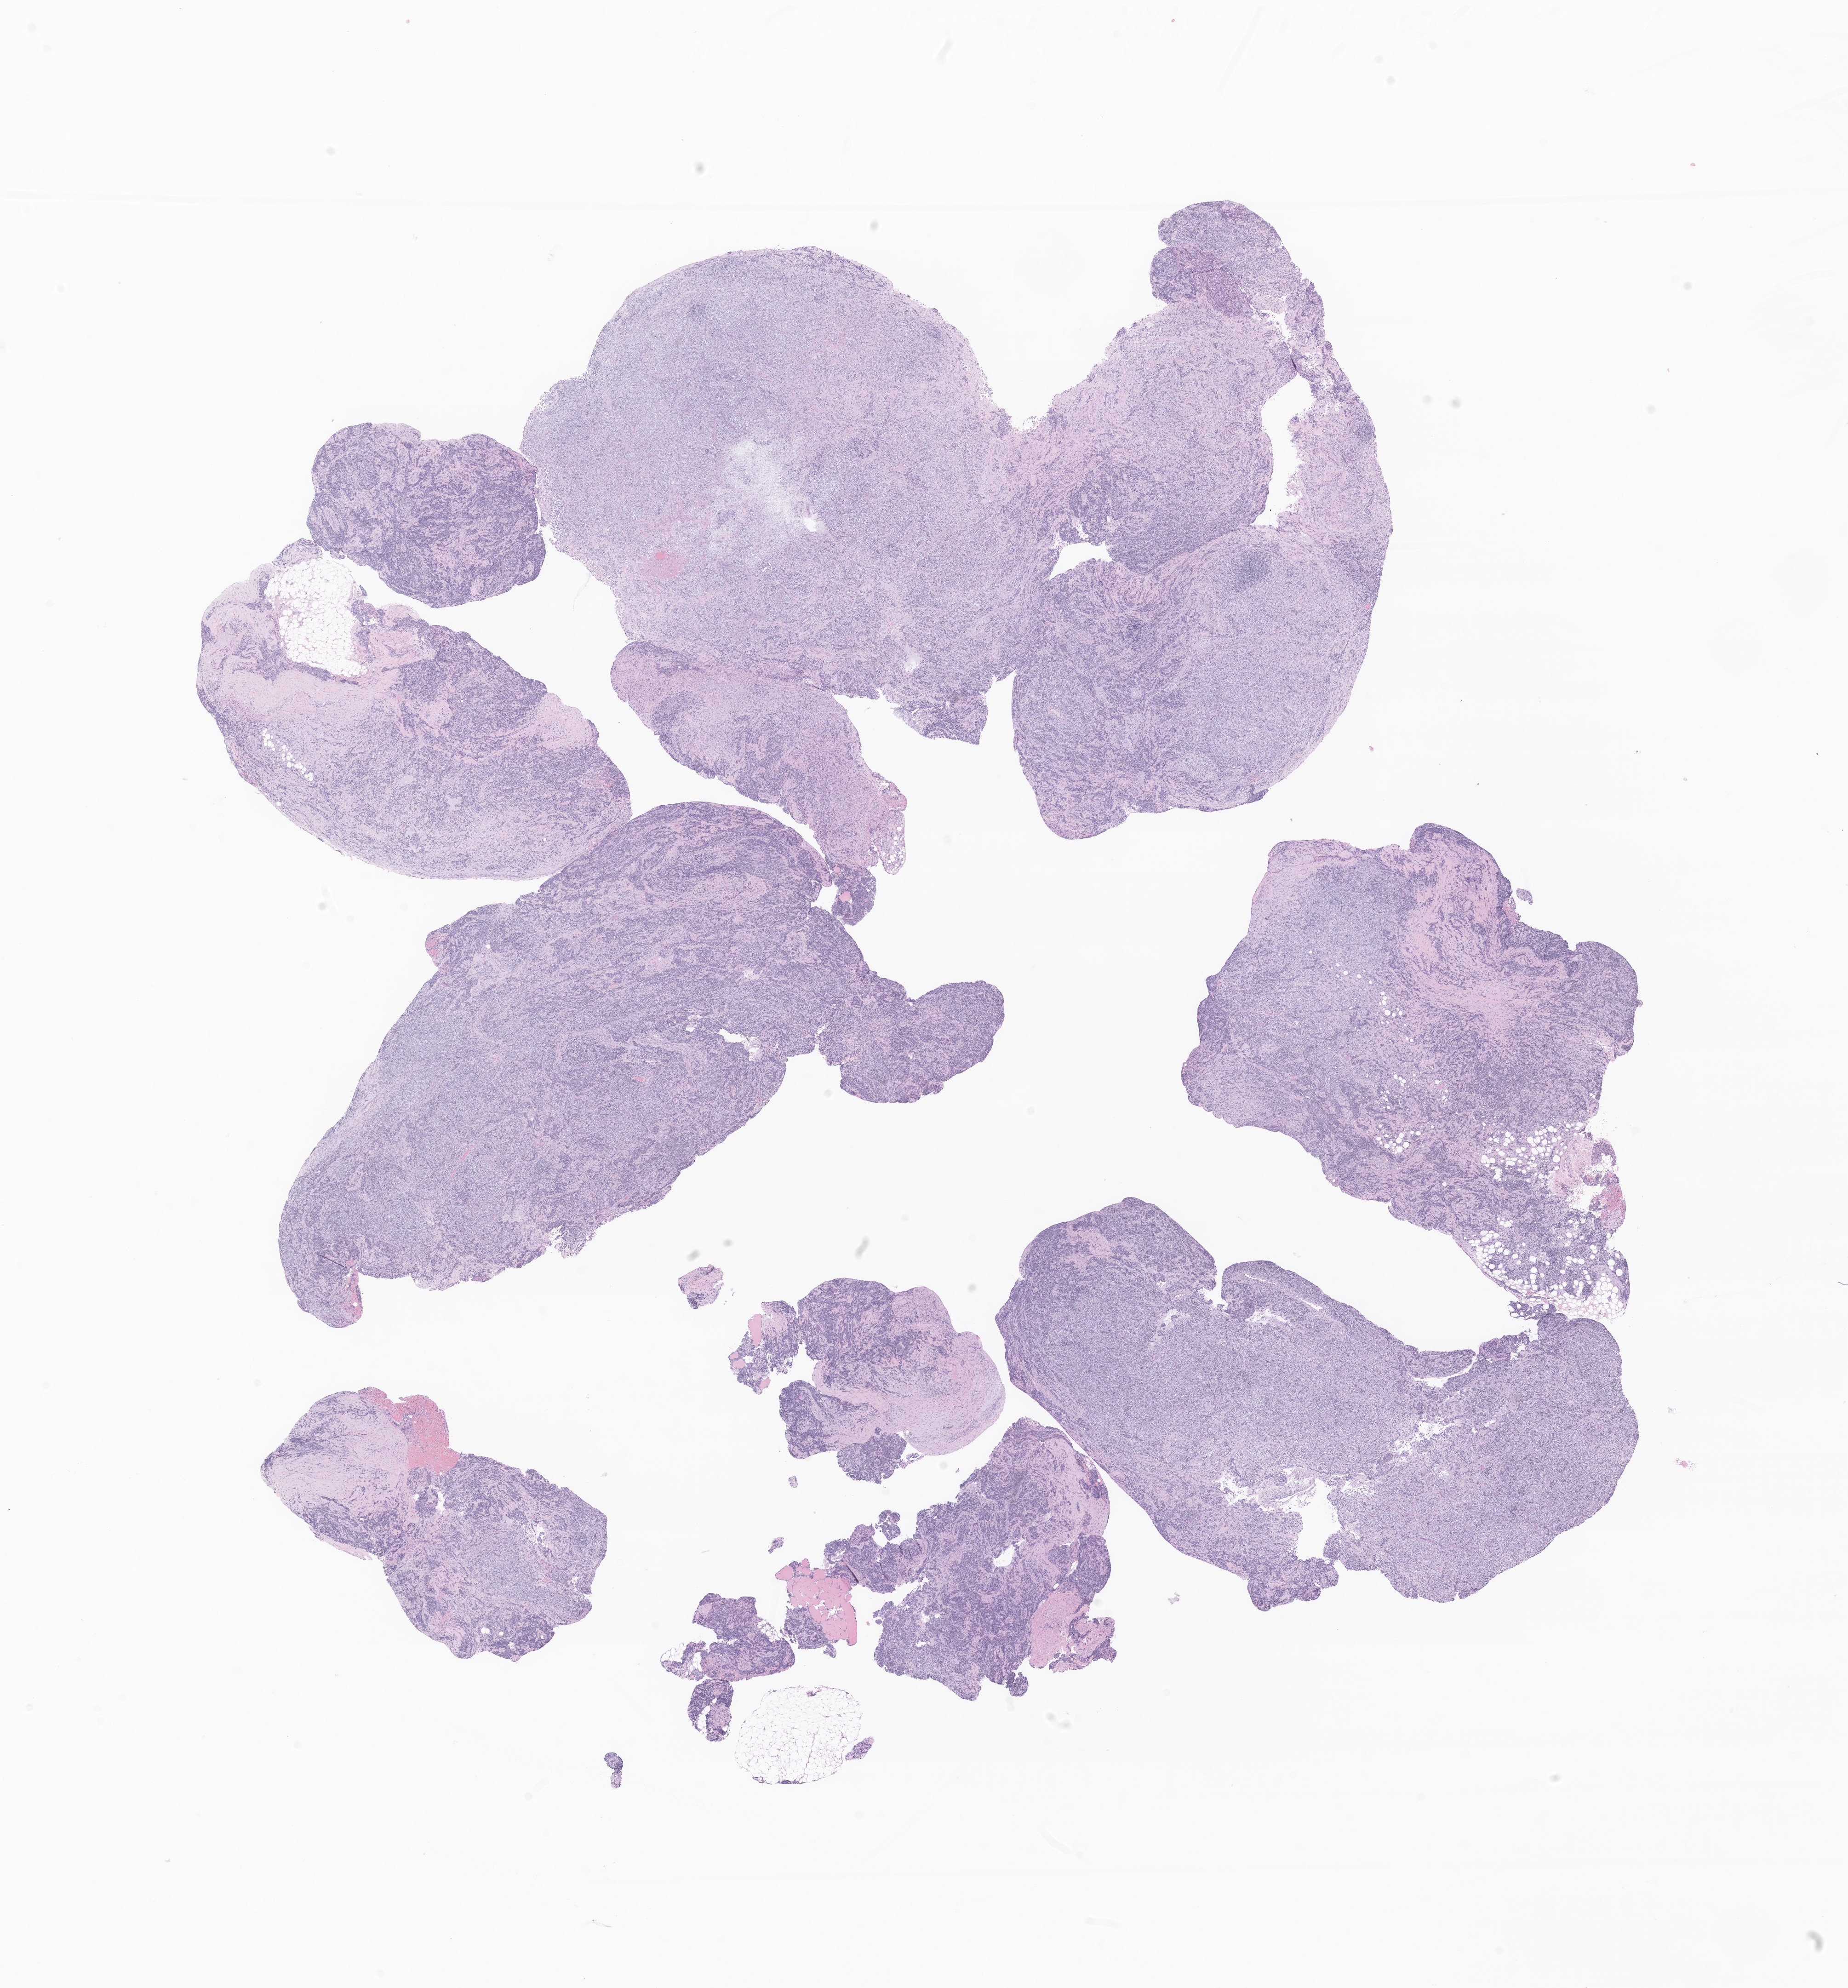
Digitized hematoxylin and eosin (H&E)-stained section of tumor tissue from the orbit, a low-resolution overview of the entire scanned area, about 16.9 x 18.2 mm. Formalin-fixed, paraffin-embedded (FFPE) tissue. Female patient, age 168 months (14 years).
Diagnosis: Rhabdomyosarcoma, NOS.